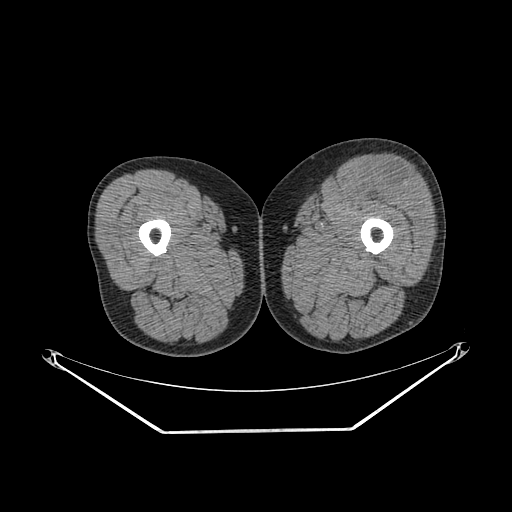
CT of an extremity soft-tissue mass (from a PET/CT study), one axial slice. Position 225 of 267 along the scan axis. 140 kVp. Soft-tissue window (W 400 / L 40 HU). 512 × 512 image matrix, field of view 500 × 500 mm. Male patient. From the clinical record (not read from this slice): histological type: extraskeletal osteosarcoma; grade: high; site of the primary tumour: thigh.
Structures marked on this image (expert contour drawn on MRI and transferred to this co-registered scan by the dataset authors):
- gross tumour volume (mass): bounding box [x1, y1, x2, y2] px = [370, 165, 419, 207]